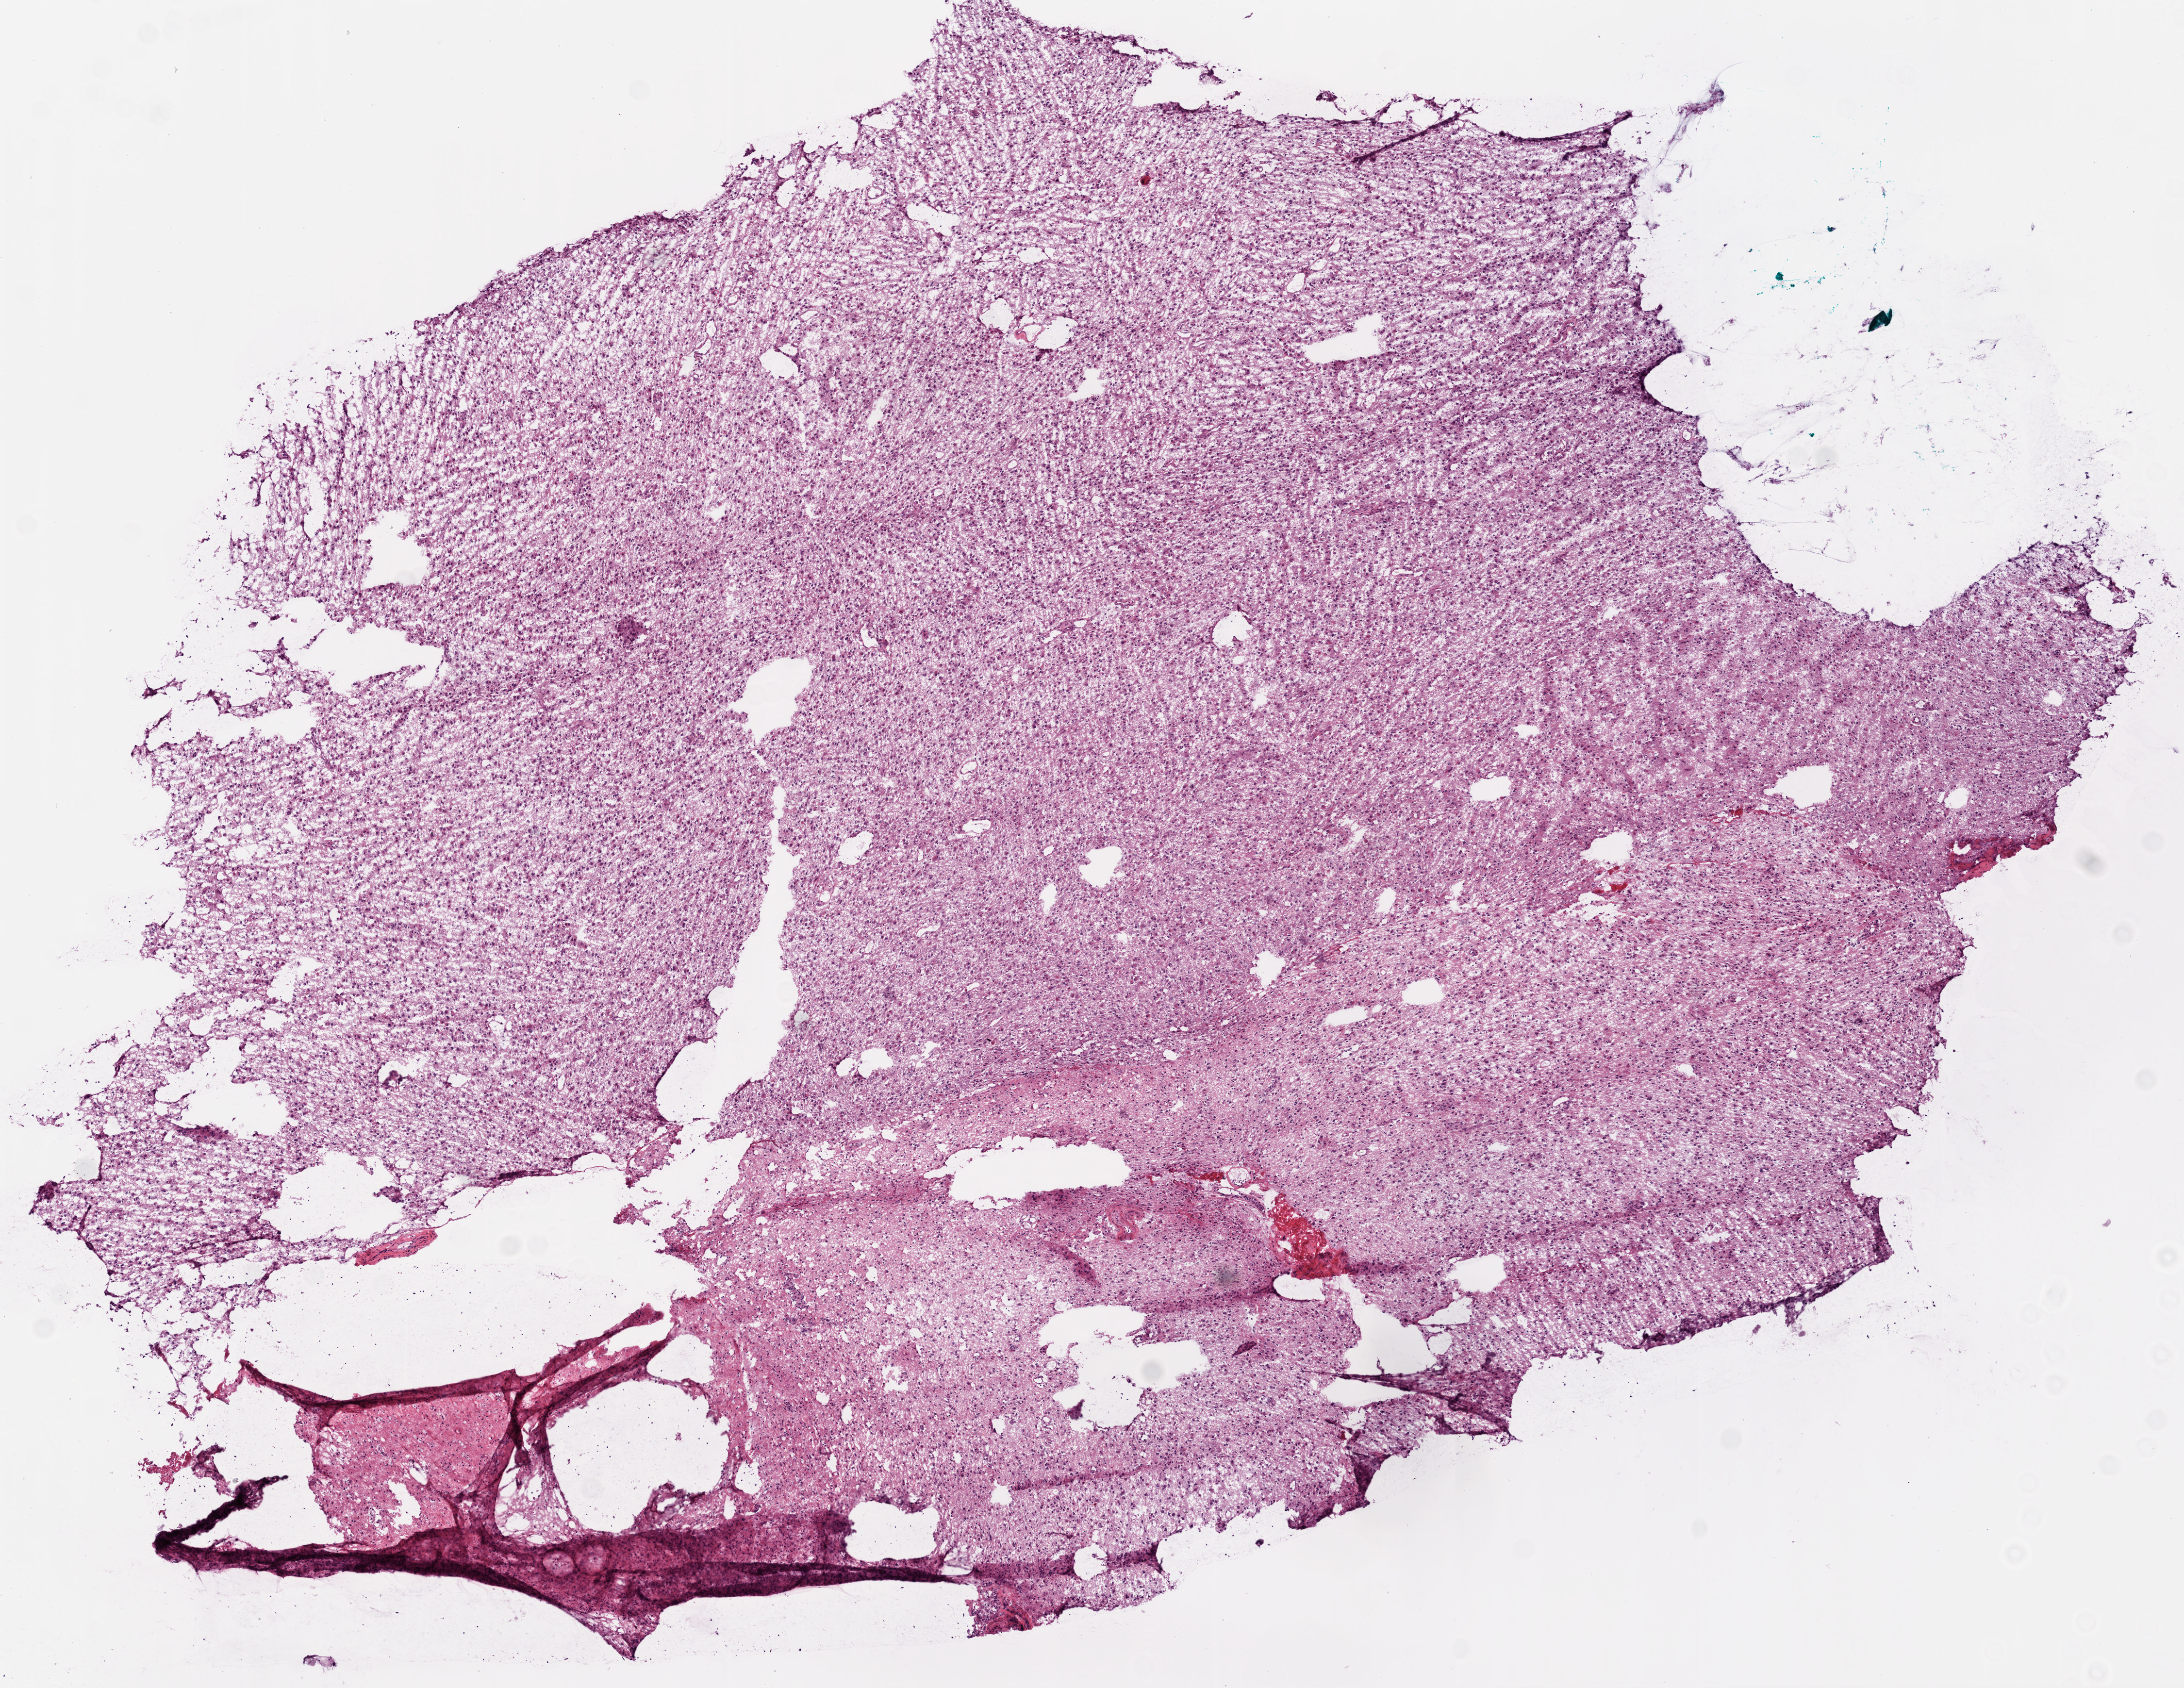
Digitized H&E-stained tissue section (whole slide), a low-resolution overview of the entire scanned area, about 9.0 x 7.0 mm (from a 20x scan). Frozen section from the bottom of the tissue portion. Sample: primary tumour, brain. Female, age 36 years at initial diagnosis. Slide review estimates, as recorded: tumour cells 100%, tumour nuclei 95%.
Histologic diagnosis: Glioblastoma.